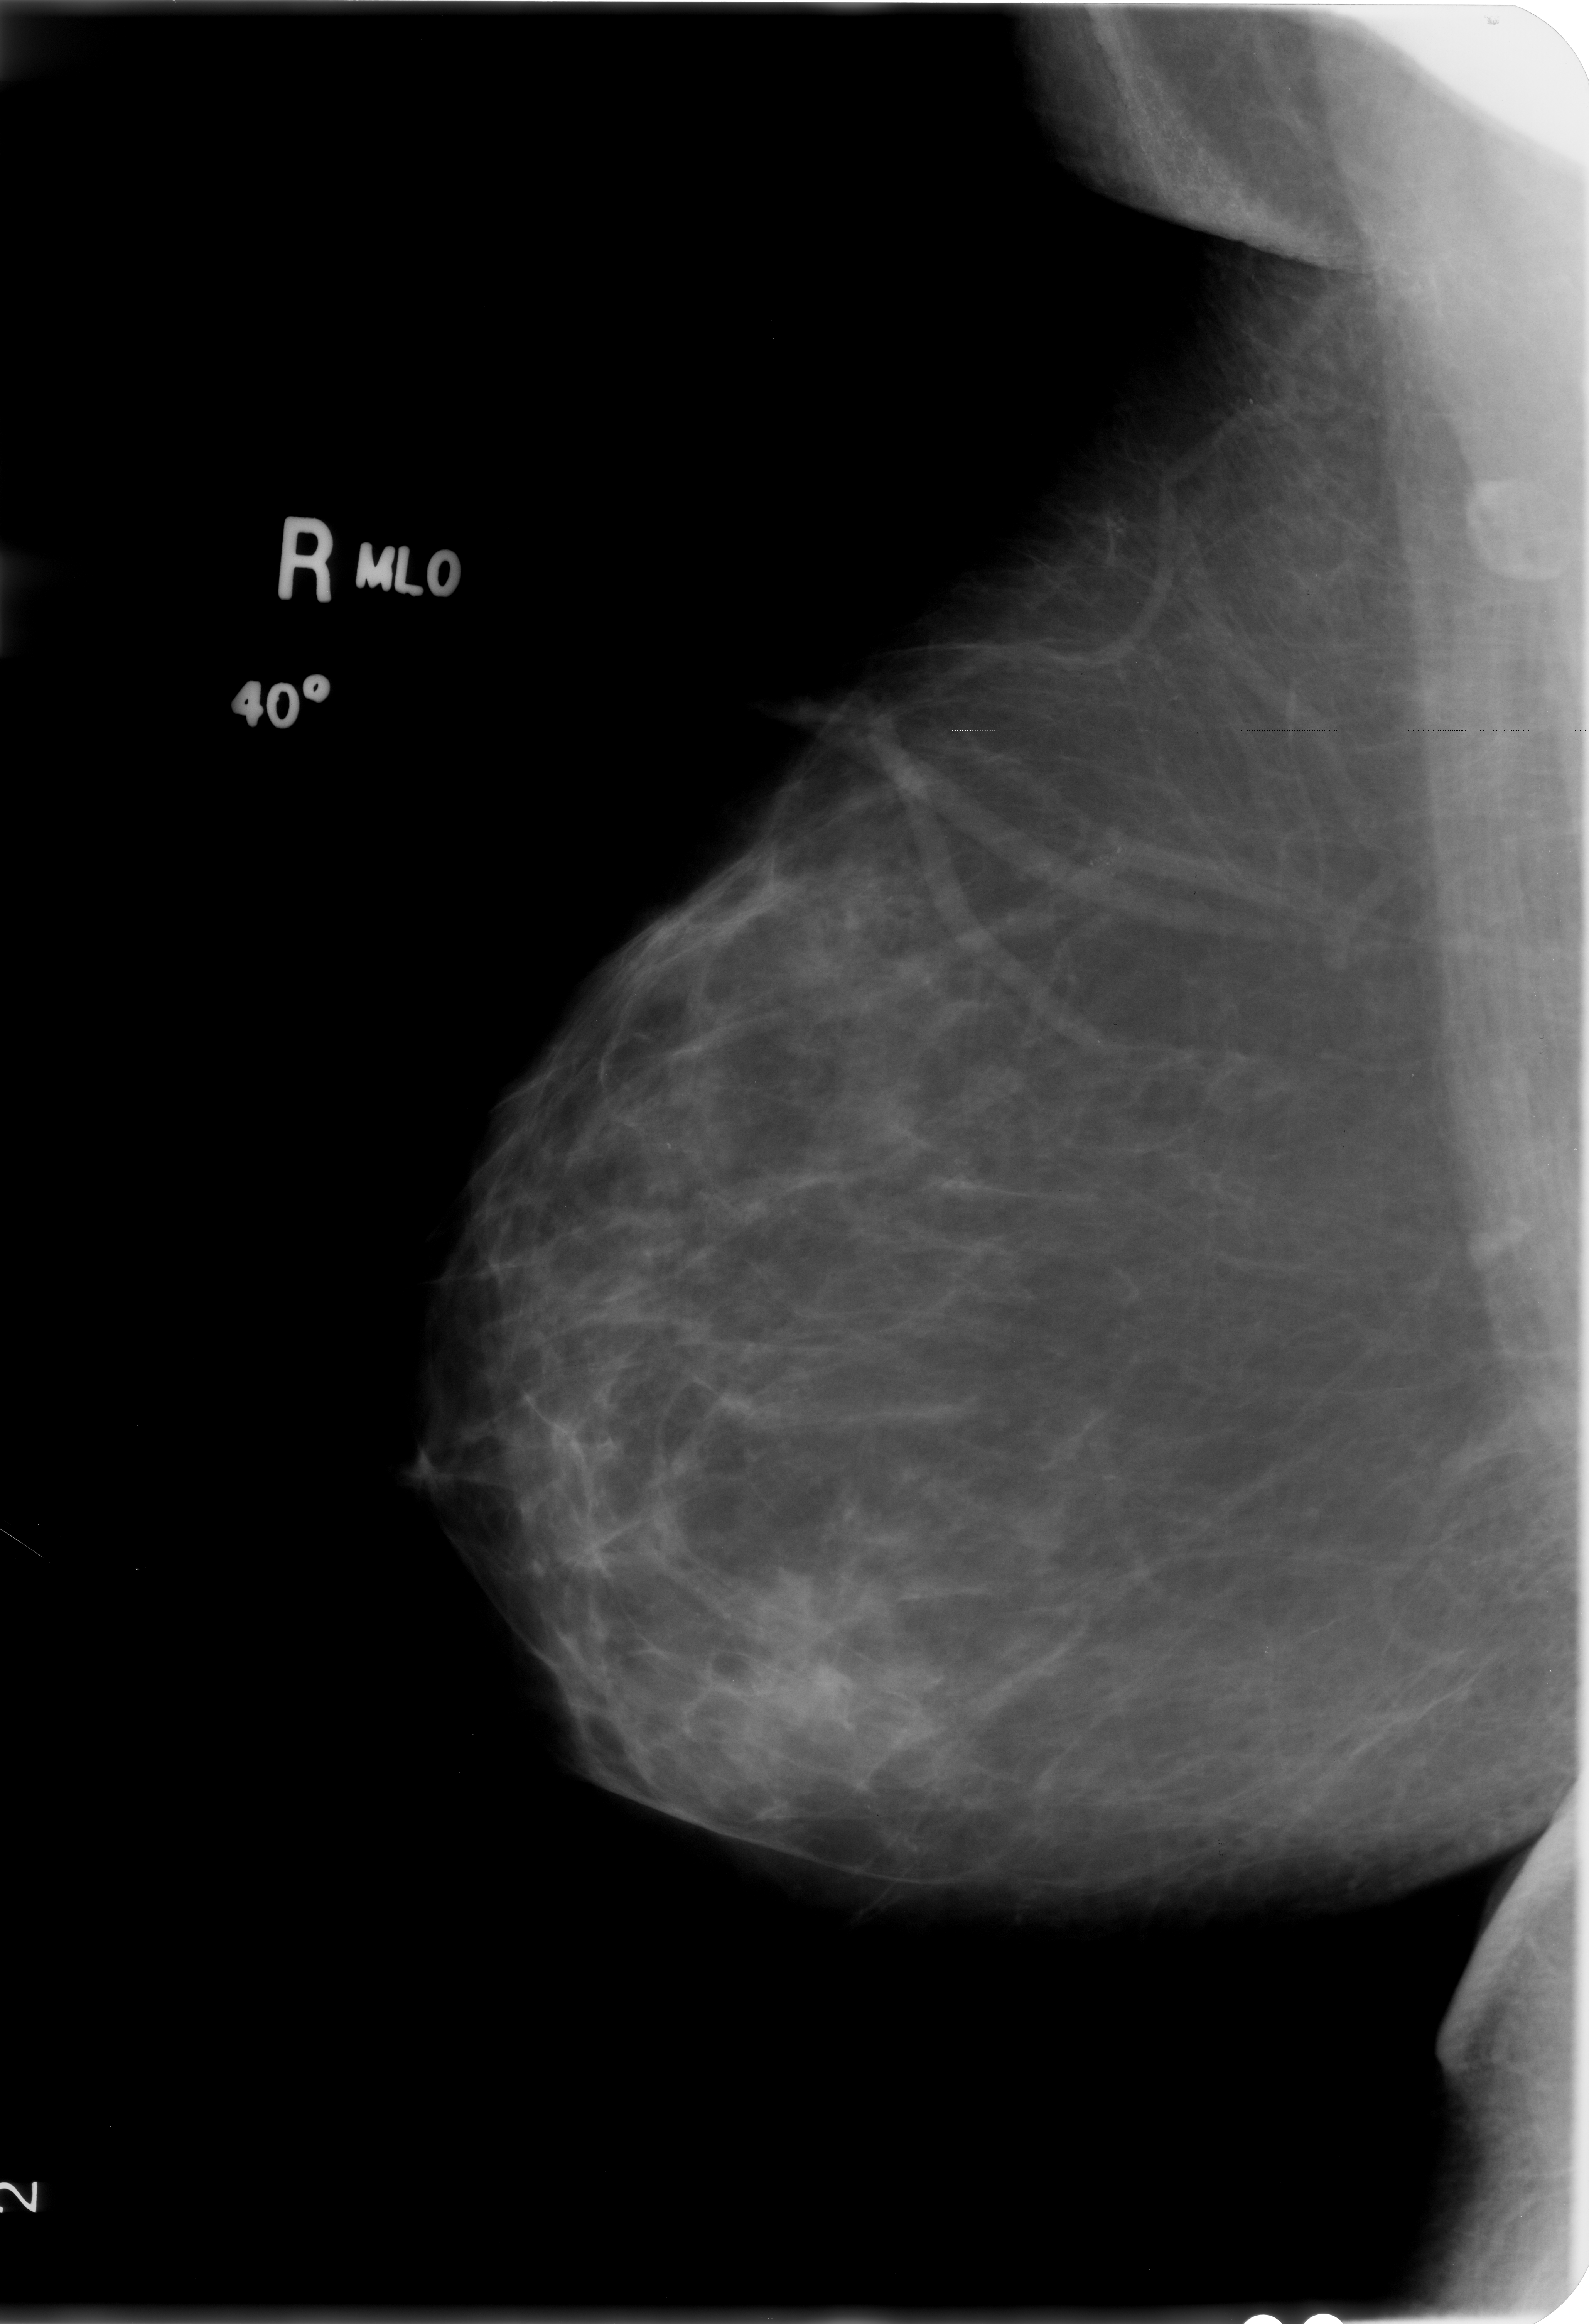
Mammogram (digitized film). Right breast. MLO view. Breast composition: almost entirely fatty (BI-RADS density category 1 of 4). 1589 × 2324 image matrix.
Marked abnormalities (boxes around the expert regions of interest):
- calcifications, morphology pleomorphic, distribution clustered; BI-RADS assessment category 4; pathology (as recorded): benign: bounding box <1039,811,1155,911> (left, top, right, bottom; pixels)